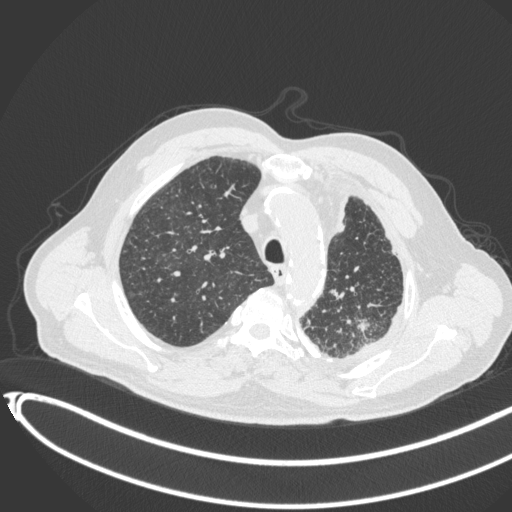
Chest CT, one axial slice; position 333 of 451 along the scan axis; reconstruction kernel B31f; lung window (W 1500 / L -600 HU); 1 mm slice thickness; 512 × 512 image matrix, field of view 400 × 400 mm. Patient: male, 78 years. Case-level facts recorded for this patient, not image findings: clinical TNM (as recorded): T1c N0 M1.
Structures marked on this image (rectangle marked by the reading radiologist):
- lung tumour (recorded histology: adenocarcinoma): box from (x=355, y=313) to (x=376, y=339) px